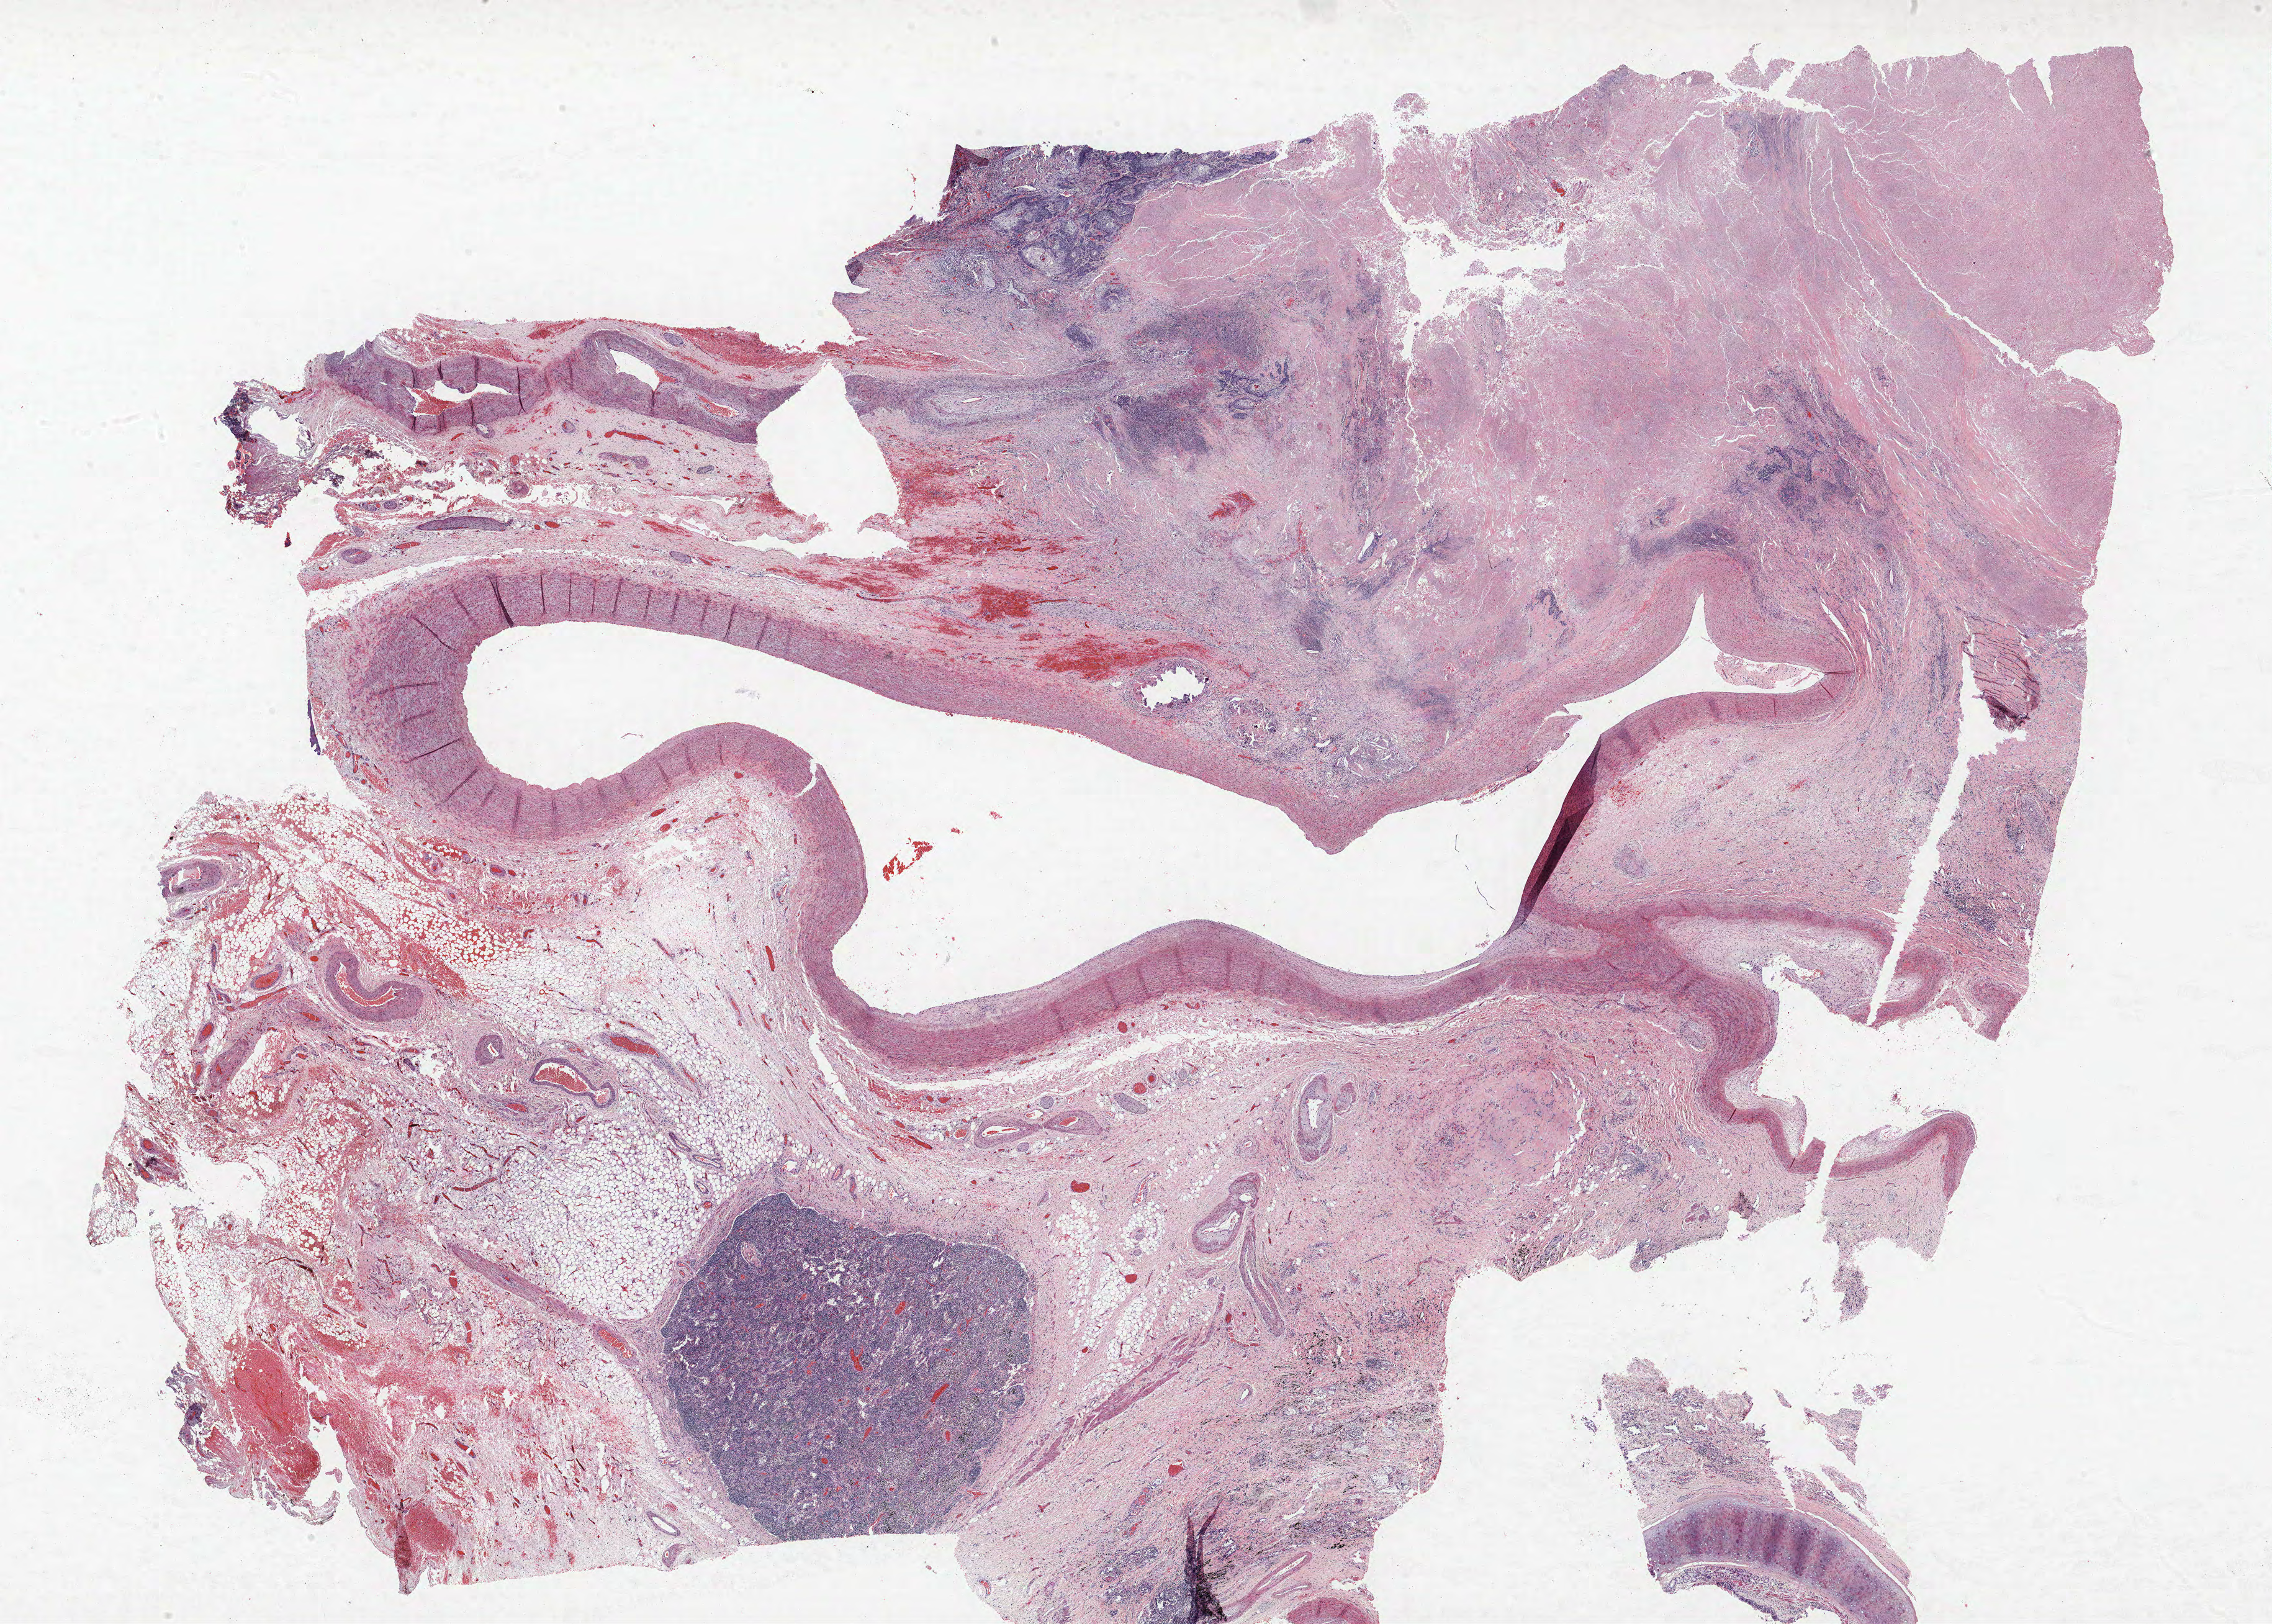
Whole-slide histology image, Hematoxylin and eosin (H&E) stained — a low-resolution overview of the entire scanned area, about 29.3 x 20.9 mm (acquisition: 40x scan). FFPE section. Lung. Male patient, aged 62 at enrolment. Current smoker at enrolment. Grade: cannot be assessed (GX).
Participant's lung-cancer diagnosis: Squamous cell carcinoma, NOS. Tumour size (pathology): 35 mm. ICD-O-3 topography: main bronchus (C34.0). Stage (AJCC 6th edition): IB. Primary tumour location (clinical record): left main stem bronchus.